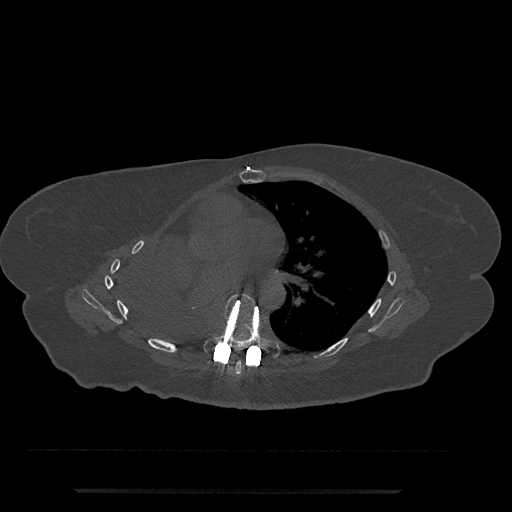
CT including the spine, one axial slice; slice 451 of 797 in the series (ordered by position); reconstruction kernel Br40s/3; 120 kVp; bone window (W 1800 / L 400 HU); 512 × 512 image matrix, field of view 440 × 440 mm. Female patient, age 51 years. From the clinical record (not read from this slice): primary cancer: neuro.
Annotated regions visible in this slice (semi-automatically segmented with operator editing):
- T6 vertebra: bounding box (x1, y1, x2, y2) in pixels: (220, 360, 242, 377)
- T7 vertebra: (203, 294, 280, 357)